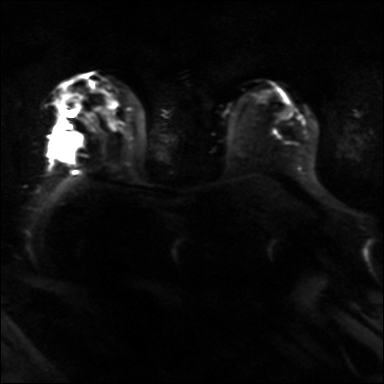
Breast MRI, one axial slice. Diffusion-weighted series; image 2 of 4 stored at this slice position (different b-values; order by instance number). 3 T. 384 × 384 image matrix. Female patient.
Annotated regions visible in this slice (expert manual segmentation):
- tumour on diffusion-weighted imaging: bounding box <49,131,79,162> (left, top, right, bottom; pixels)